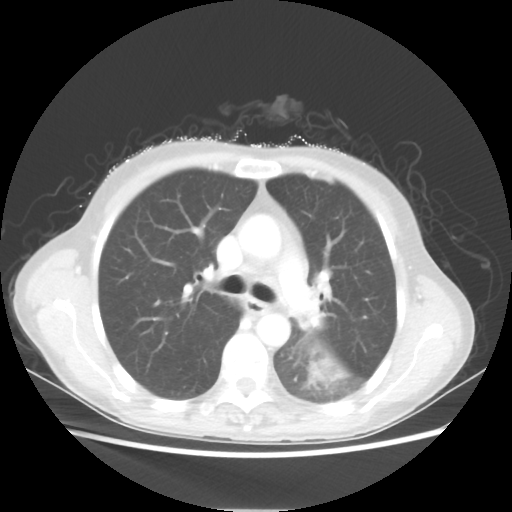
Chest CT, one axial slice. Position 35 of 56 along the scan axis. Reconstruction kernel STANDARD. Lung window (W 1500 / L -600 HU). 5 mm slice thickness. 512 × 512 image matrix. Patient: female, 53 years. Case-level facts recorded for this patient, not image findings: clinical TNM (as recorded): T3 N0 M0.
Annotated regions visible in this slice (bounding box drawn by a radiologist):
- lung tumour (recorded histology: adenocarcinoma): bounding box <308,359,343,384> (left, top, right, bottom; pixels)